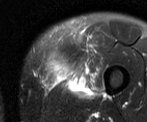
MRI of an extremity soft-tissue mass, one axial slice. Position 11 of 52 along the scan axis. T2-weighted fat-saturated. MR volume resampled by the dataset authors to the PET/CT grid (not the native acquisition matrix). 3.27 mm slice thickness. 147 × 122 image matrix, field of view 144 × 119 mm. Male patient. Case-level facts recorded for this patient, not image findings: histological type: pleiomorphic liposarcoma; grade: high; site of the primary tumour: left thigh.
Outlined on this slice (expert contour drawn on MRI and transferred to this co-registered scan by the dataset authors):
- gross tumour volume including surrounding oedema: box from (x=46, y=50) to (x=97, y=95) px
- gross tumour volume (mass): (x=46, y=50)–(x=72, y=81)